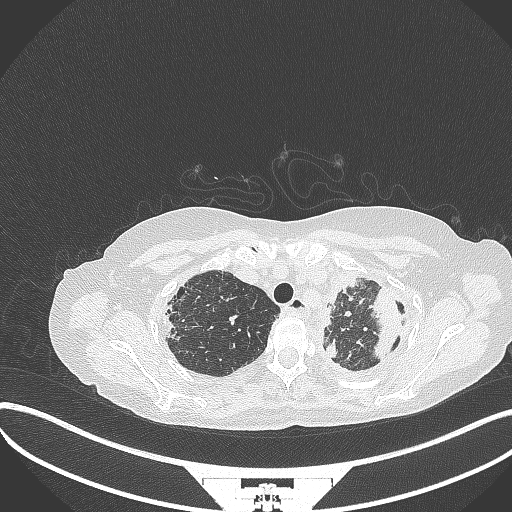
Chest CT, one axial slice. Slice 285 of 373 in the series (ordered by position). Reconstruction kernel B70f. 120 kVp. Lung window (W 1500 / L -600 HU). 1 mm slice thickness. 512 × 512 image matrix, field of view 400 × 400 mm. Patient: female, 56 years. Case-level facts recorded for this patient, not image findings: clinical TNM (as recorded): T1 N0 M0.
Outlined on this slice (bounding box drawn by a radiologist):
- lung tumour (recorded histology: adenocarcinoma): bounding box <372,285,405,365> (left, top, right, bottom; pixels)